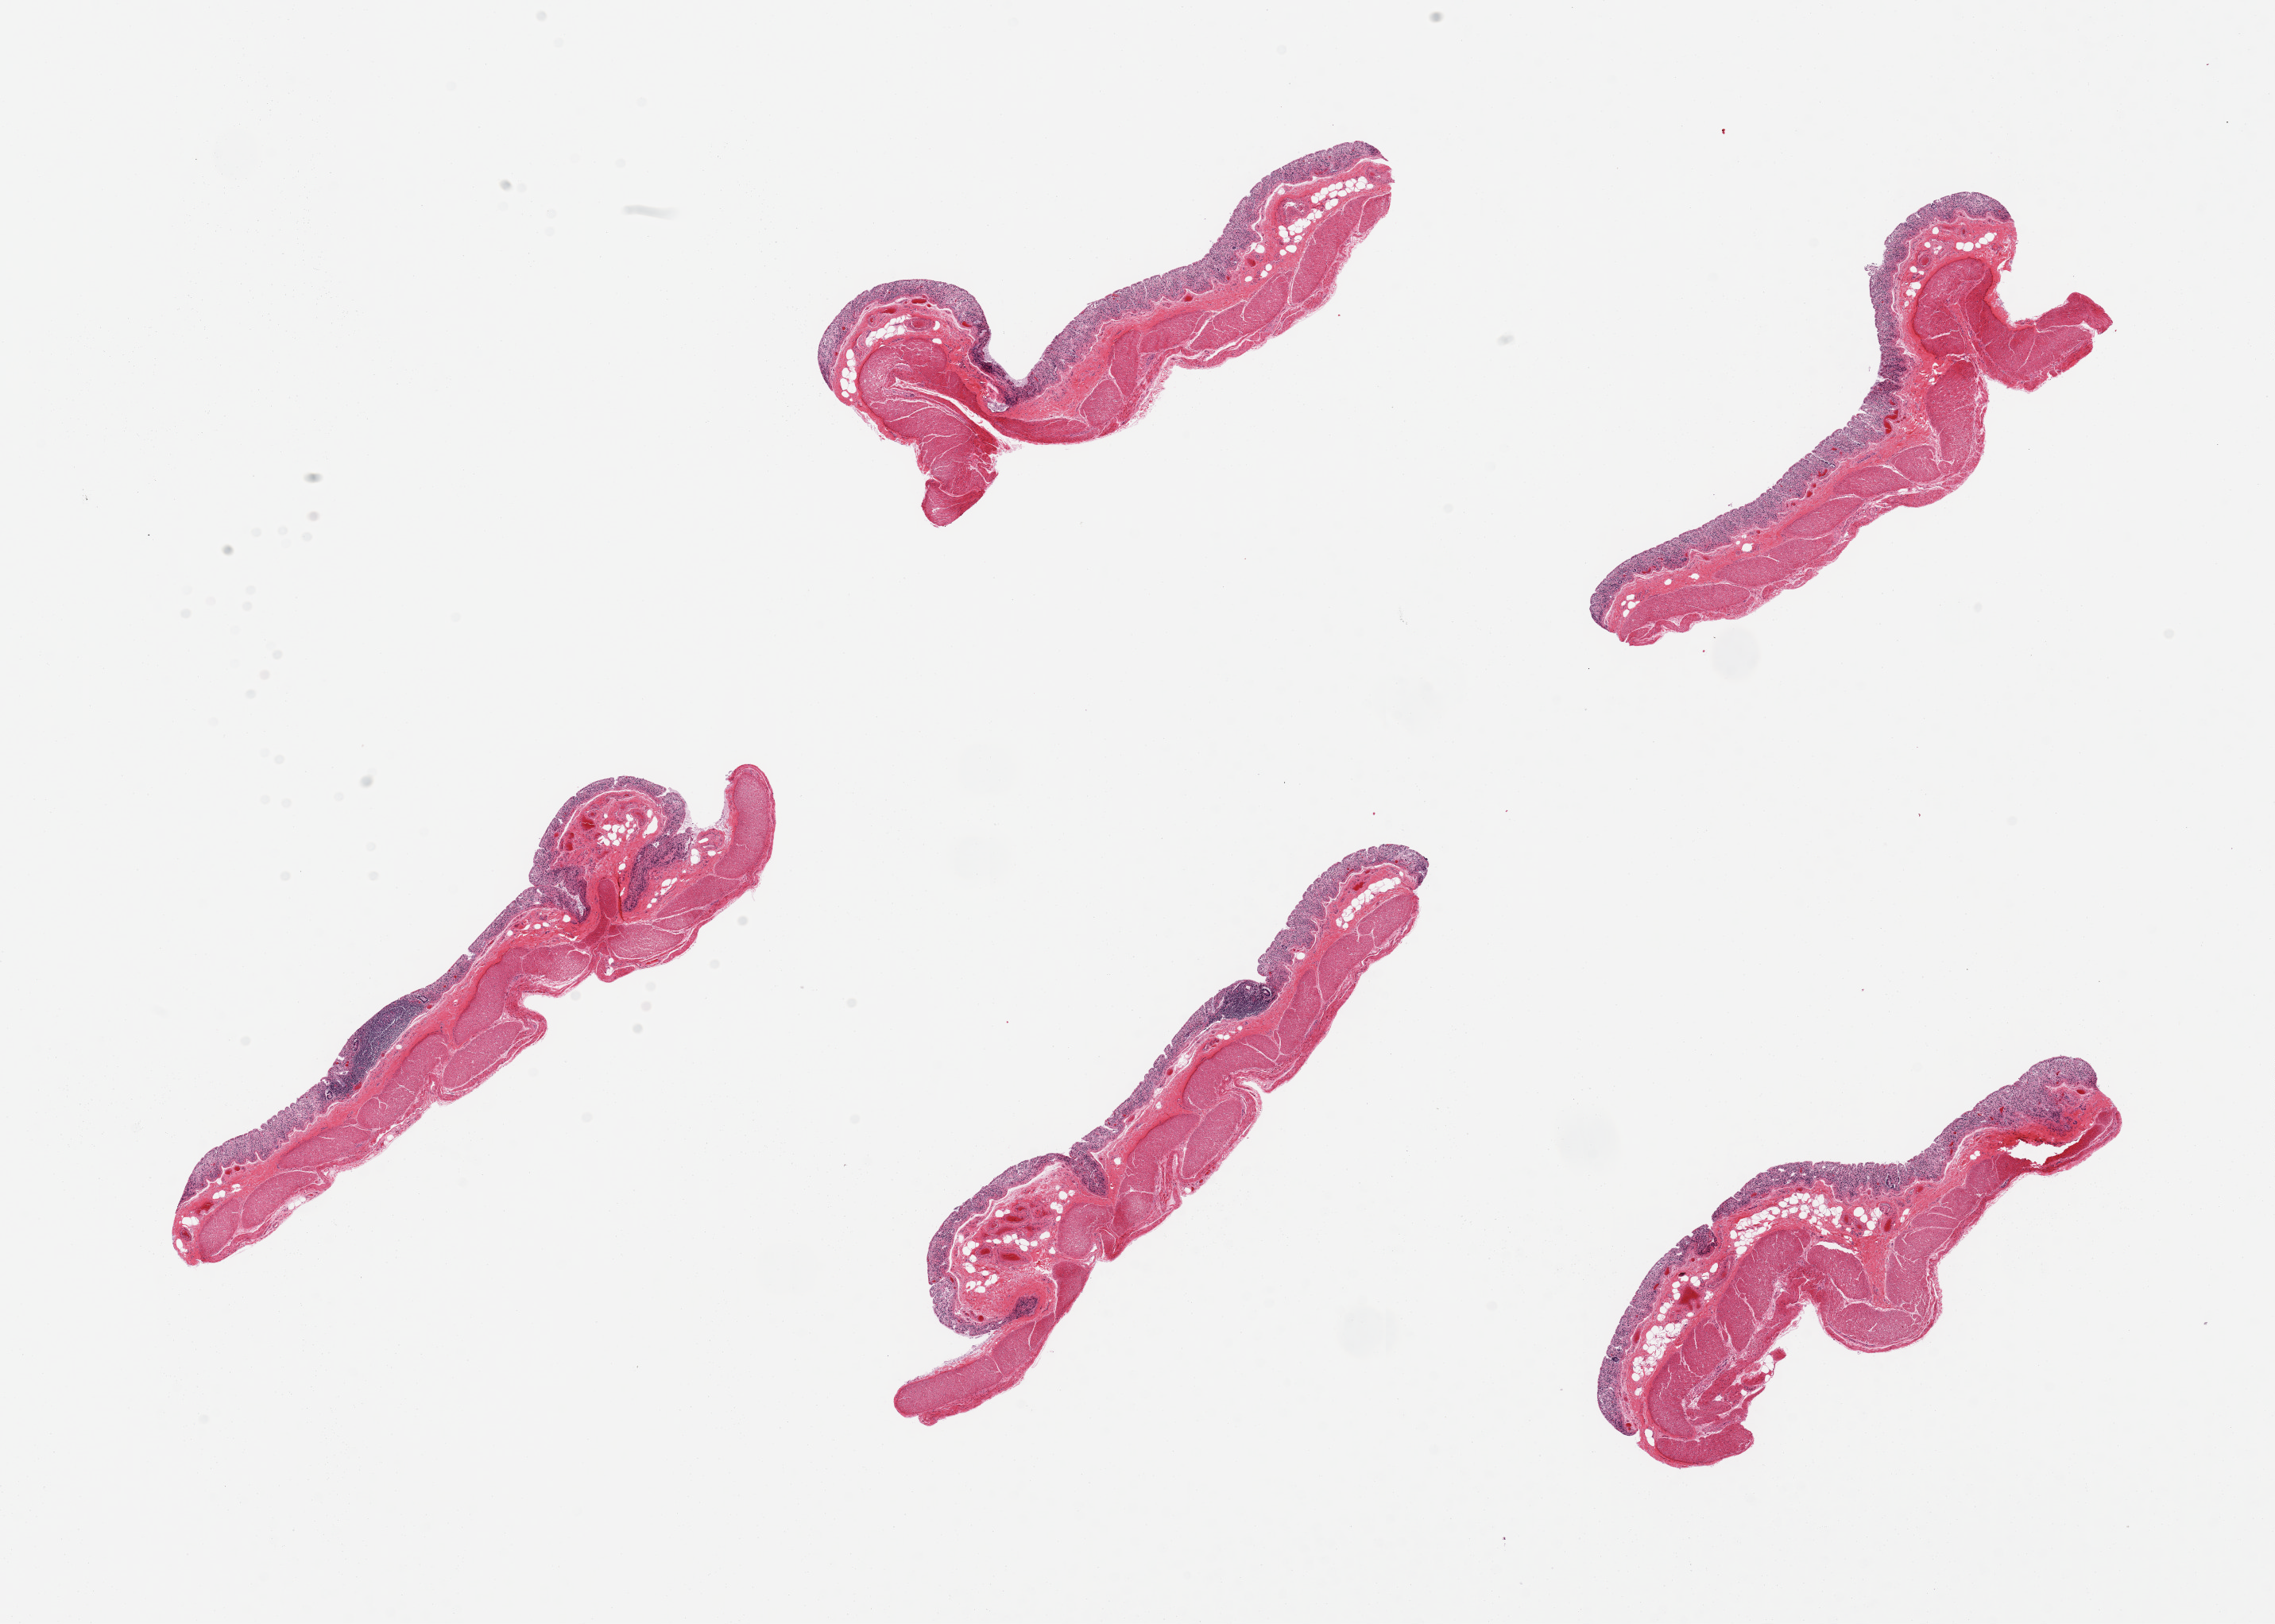
Digitized haematoxylin and eosin-stained section, a low-resolution overview of the entire scanned area, about 22.6 x 16.2 mm (from a 20x scan). PAXgene-fixed, paraffin-embedded tissue. Target tissue: transverse colon. Donor tissue sample. Donor sex: female.
Review note (as recorded): 5 pieces; mucosa is ~0.3 mm or ~30% thickness, but toally autolyzed.